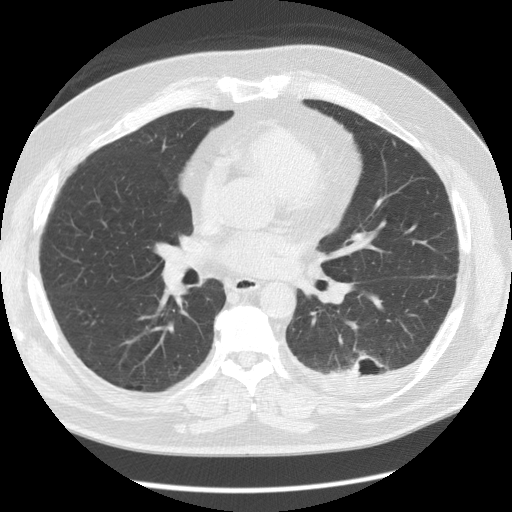
Low-dose screening chest CT, one axial slice. Slice 66 of 126 in the series (ordered by position). Reconstruction kernel STANDARD. Lung window (W 1500 / L -600 HU). 512 × 512 image matrix.
Annotated regions visible in this slice (outlined manually by an expert reader):
- lesion 1 (tumor, lower lobe of left lung): bounding box <345,355,368,376> (left, top, right, bottom; pixels)